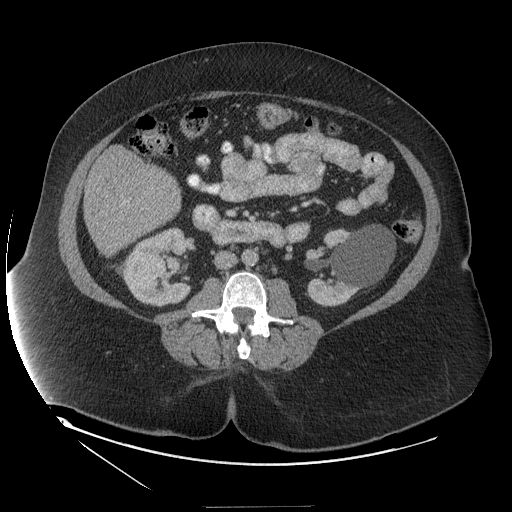
Contrast-enhanced abdominal CT (liver protocol), one axial slice; position 39 of 127 along the scan axis; reconstruction kernel STANDARD; soft-tissue window (W 400 / L 40 HU); 512 × 512 image matrix. From the clinical record (not read from this slice): diagnosis: hepatocellular carcinoma (patient treated with transarterial chemoembolisation; whether this scan precedes or follows treatment is not stated here); TNM stage (as recorded): Stage-II; Child-Pugh class: A; tumour nodularity: multinodular; tumour size: 3 cm.
Outlined on this slice (semi-automatically segmented with operator editing):
- liver parenchyma outside the tumour (the mass and vessels are separate outlines, so this box may not span the whole liver): bounding box (x1, y1, x2, y2) in pixels: (84, 148, 180, 256)